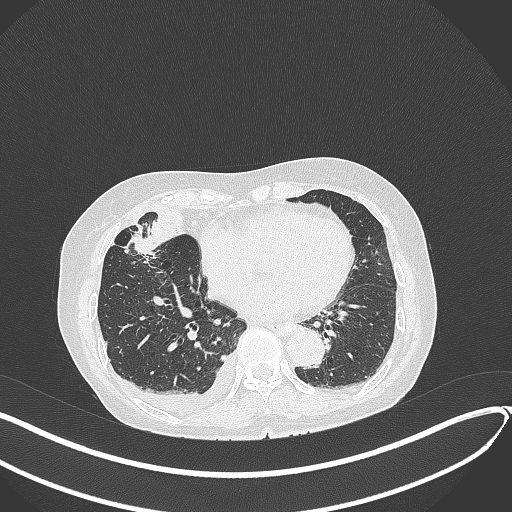
Chest CT, one axial slice. Position 141 of 418 along the scan axis. Reconstruction kernel B70f. Lung window (W 1500 / L -600 HU). 512 × 512 image matrix. Patient: female, 75 years. Case-level facts recorded for this patient, not image findings: clinical TNM (as recorded): T2a N3 M0.
Annotated regions visible in this slice (rectangle marked by the reading radiologist):
- lung tumour (recorded histology: adenocarcinoma): bounding box [x1, y1, x2, y2] px = [129, 230, 162, 258]